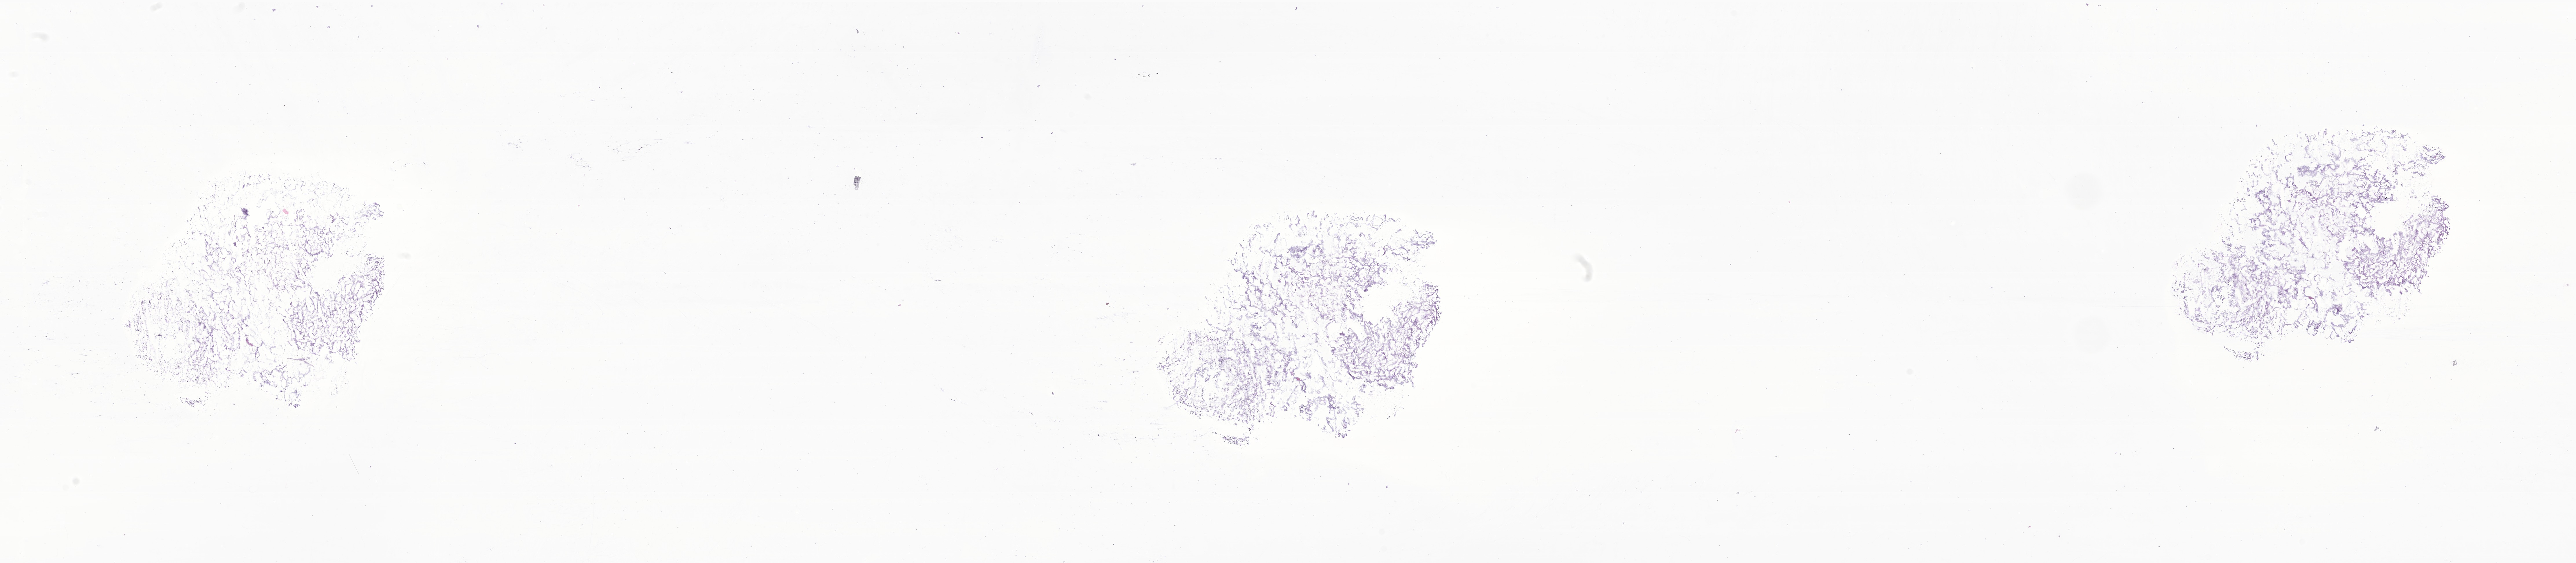
Digitized H&E-stained section of tumor tissue from the brain — shown as a low-resolution overview of the whole scanned area (about 37.5 x 8.2 mm). Frozen section (OCT-embedded). Female patient, age 56 months (4 years 8 months).
- diagnosis: Astrocytoma, NOS